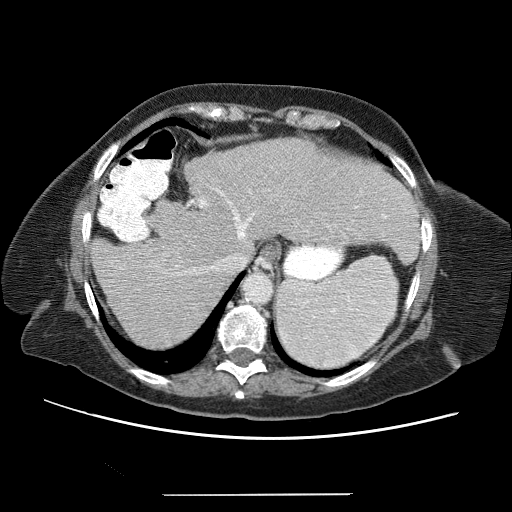
Contrast-enhanced abdominal CT (liver protocol), one axial slice. Slice 47 of 65 in the series (ordered by position). Reconstruction kernel STANDARD. Soft-tissue window (W 400 / L 40 HU). 2.5 mm slice thickness. 512 × 512 image matrix, field of view 380 × 380 mm. From the clinical record (not read from this slice): diagnosis: hepatocellular carcinoma (patient treated with transarterial chemoembolisation; whether this scan precedes or follows treatment is not stated here); TNM stage (as recorded): Stage-IIIB; Child-Pugh class: A; tumour differentiation: moderately differentiated.
Outlined on this slice (semi-automatically segmented with operator editing):
- liver parenchyma outside the tumour (the mass and vessels are separate outlines, so this box may not span the whole liver): bounding box [x1, y1, x2, y2] px = [92, 140, 419, 342]
- mass: [147, 246, 181, 280]
- liver vessels: [99, 161, 390, 299]